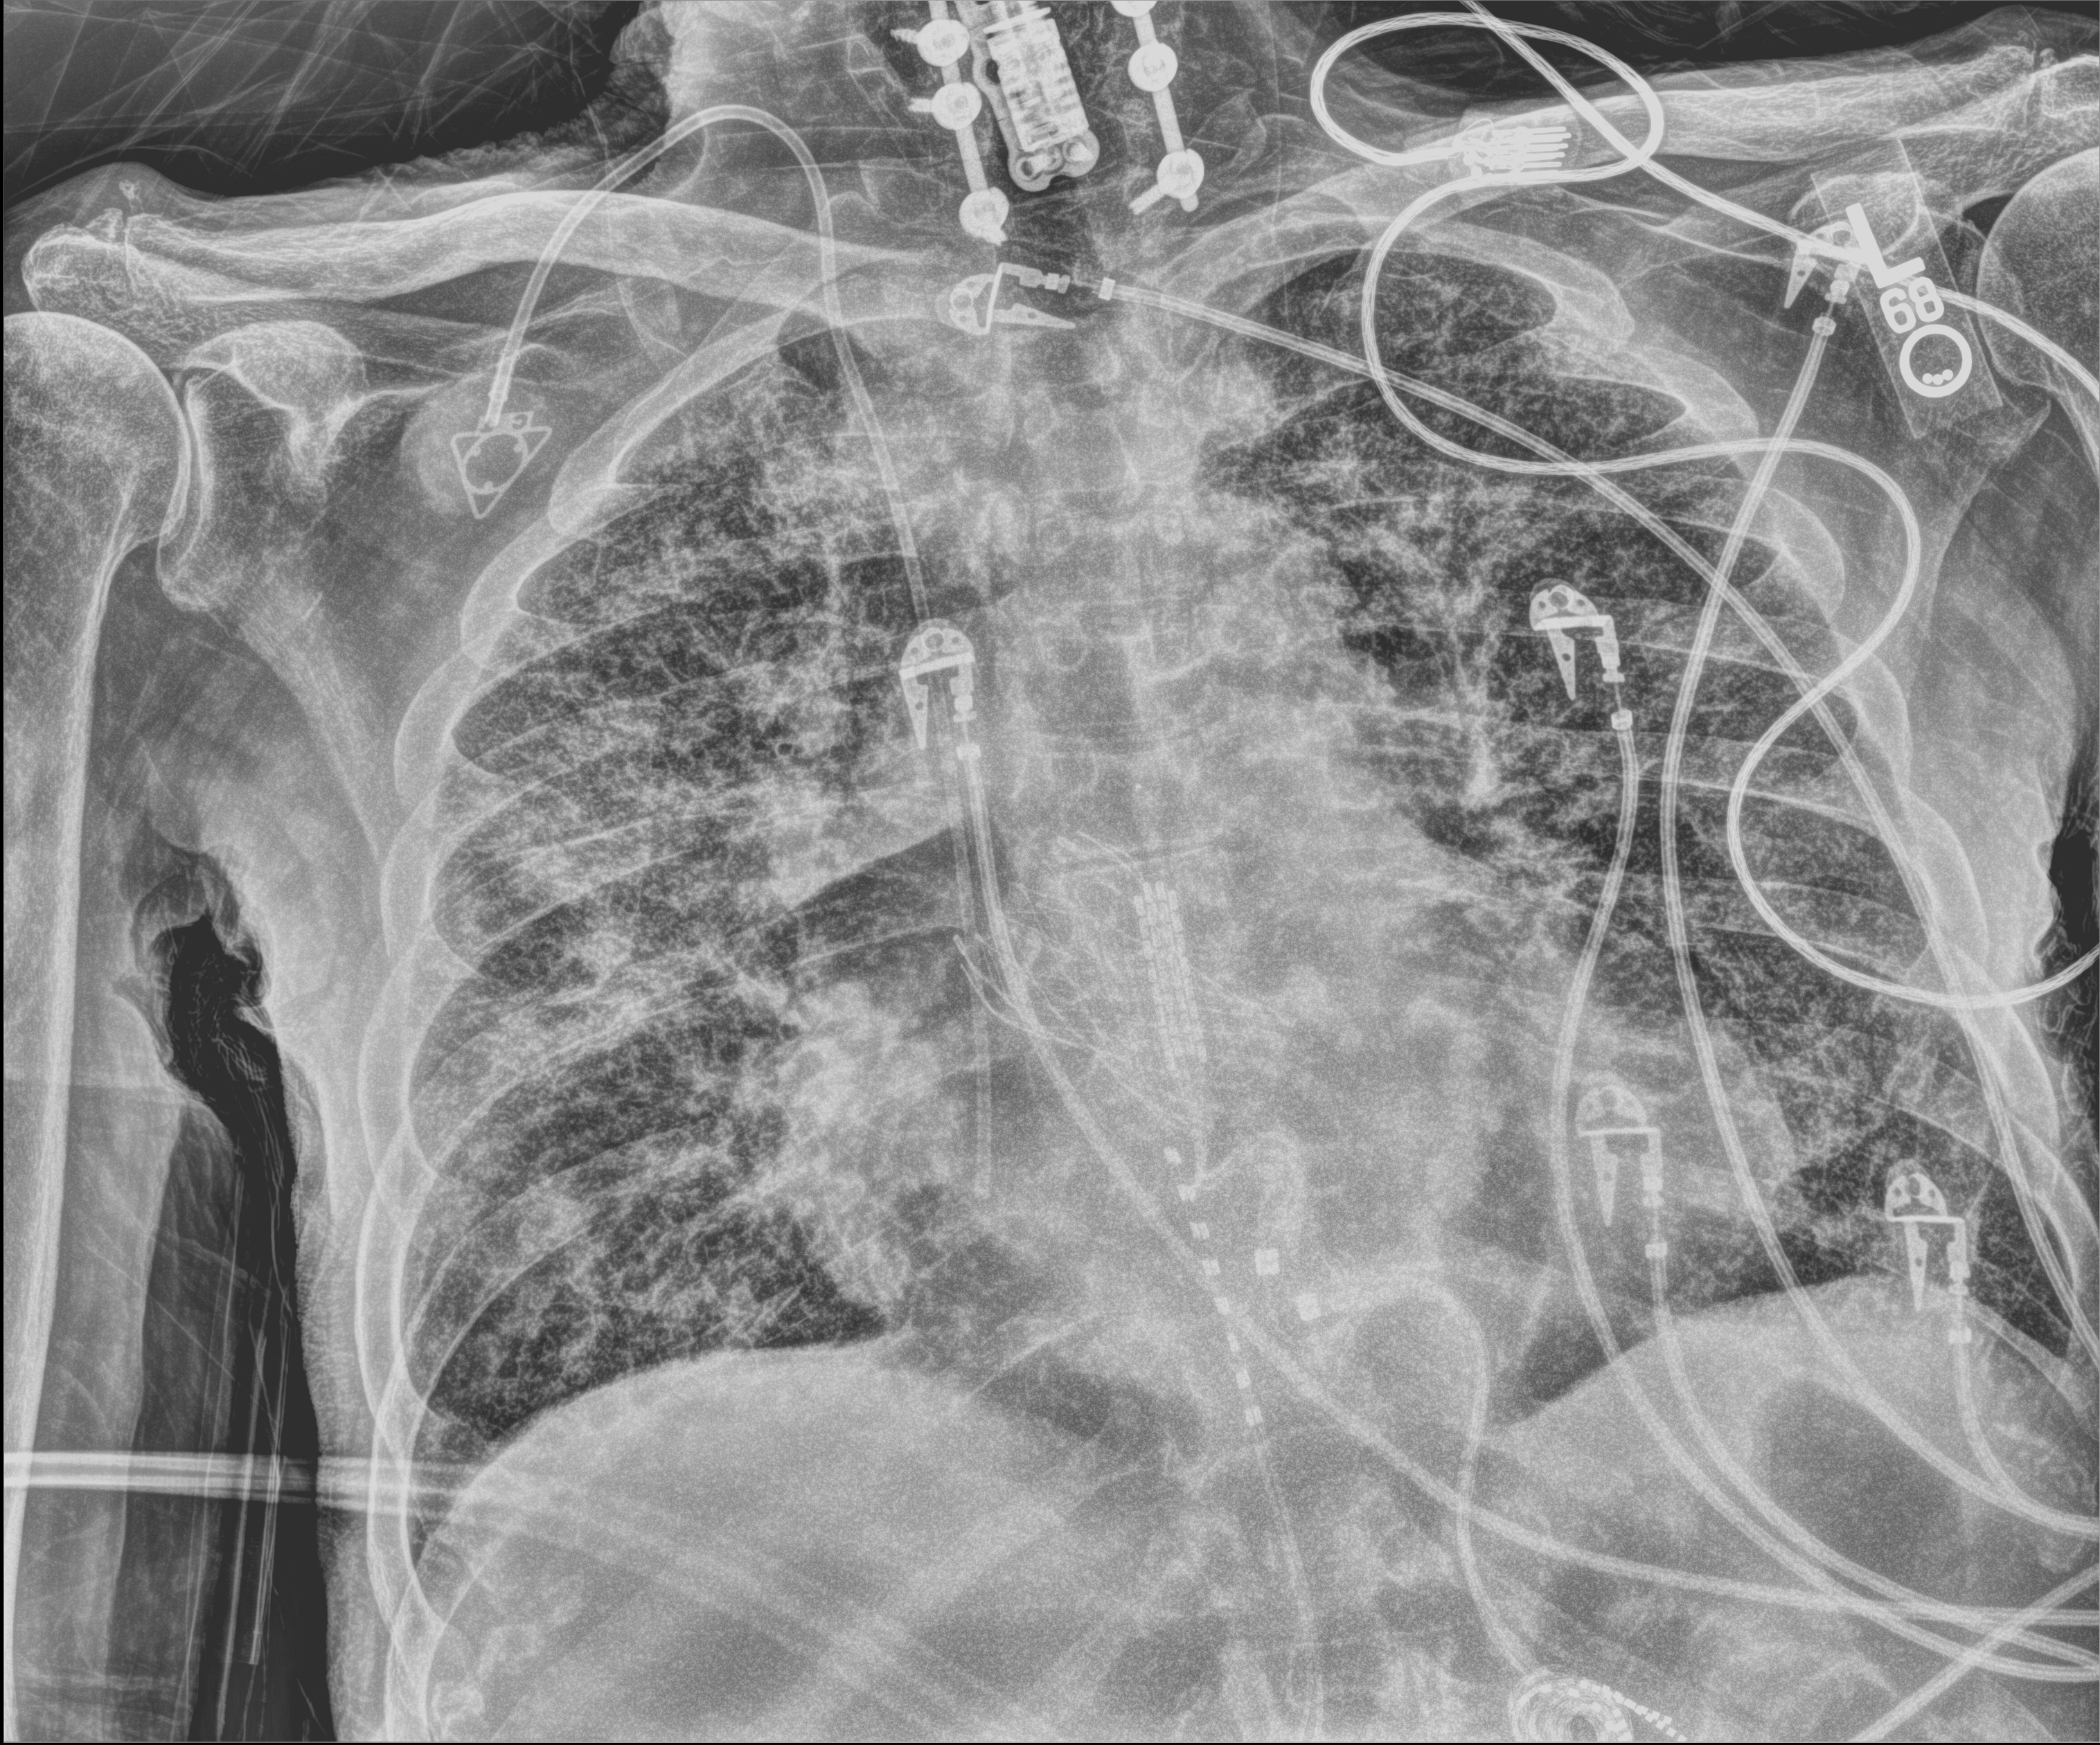
Chest X-ray, anteroposterior (AP) projection. Male patient hospitalised with COVID-19, age 75–90 years.
From the hospital-stay record, not from the radiograph (when in the stay this image was taken is not recorded): length of hospital stay: 13 days.